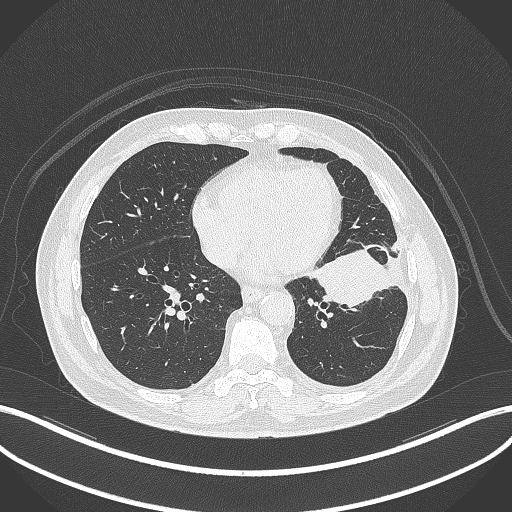
Chest CT, one axial slice; position 130 of 230 along the scan axis; reconstruction kernel B70f; 120 kVp; lung window (W 1500 / L -600 HU); 1 mm slice thickness; 512 × 512 image matrix, field of view 400 × 400 mm. Patient: male, 68 years. From the clinical record (not read from this slice): clinical TNM (as recorded): T2b N0 M0.
Structures marked on this image (bounding box drawn by a radiologist):
- lung tumour (recorded histology: squamous cell carcinoma): bounding box [x1, y1, x2, y2] px = [312, 245, 405, 308]